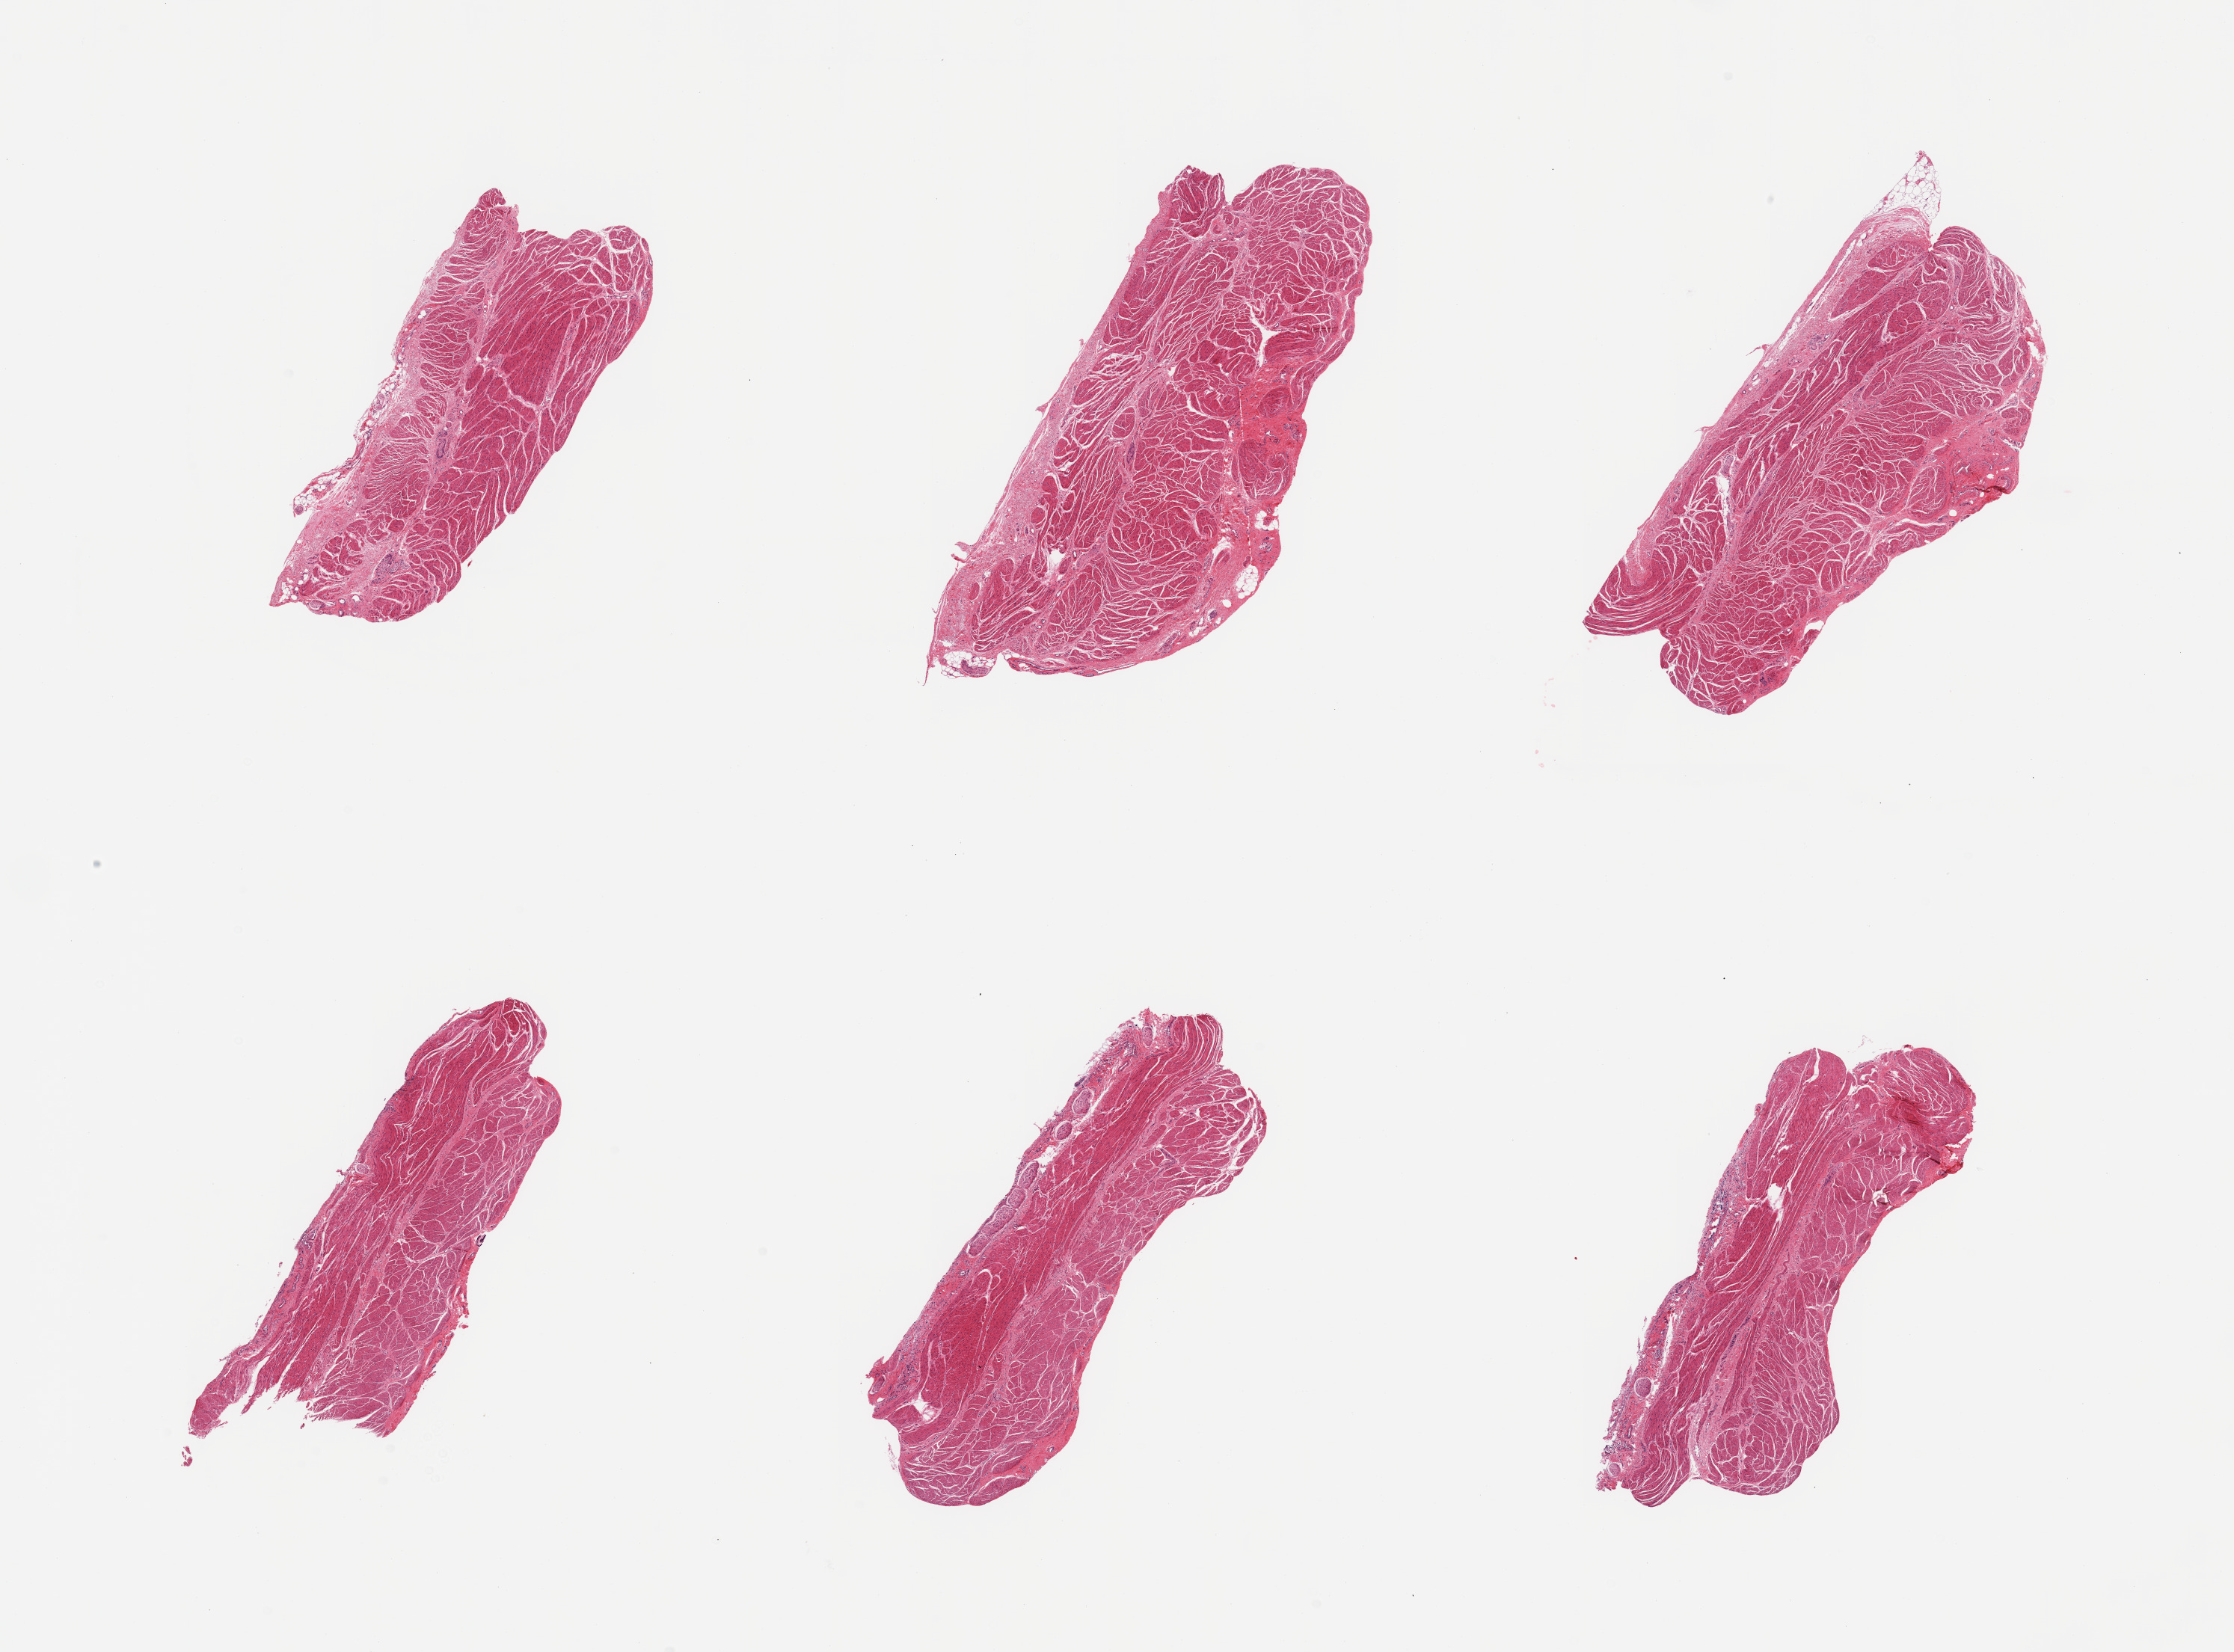
H&E whole-slide image, whole scanned area (about 23.6 x 17.5 mm, from a 20x scan) shown as a low-resolution overview, PAXgene-fixed paraffin-embedded (PFPE) section, section of gastroesophageal junction (target tissue), tissue donor sample. Donor: female.
Pathologist's review note for this sample: 6 pieces; well trimmed muscle.